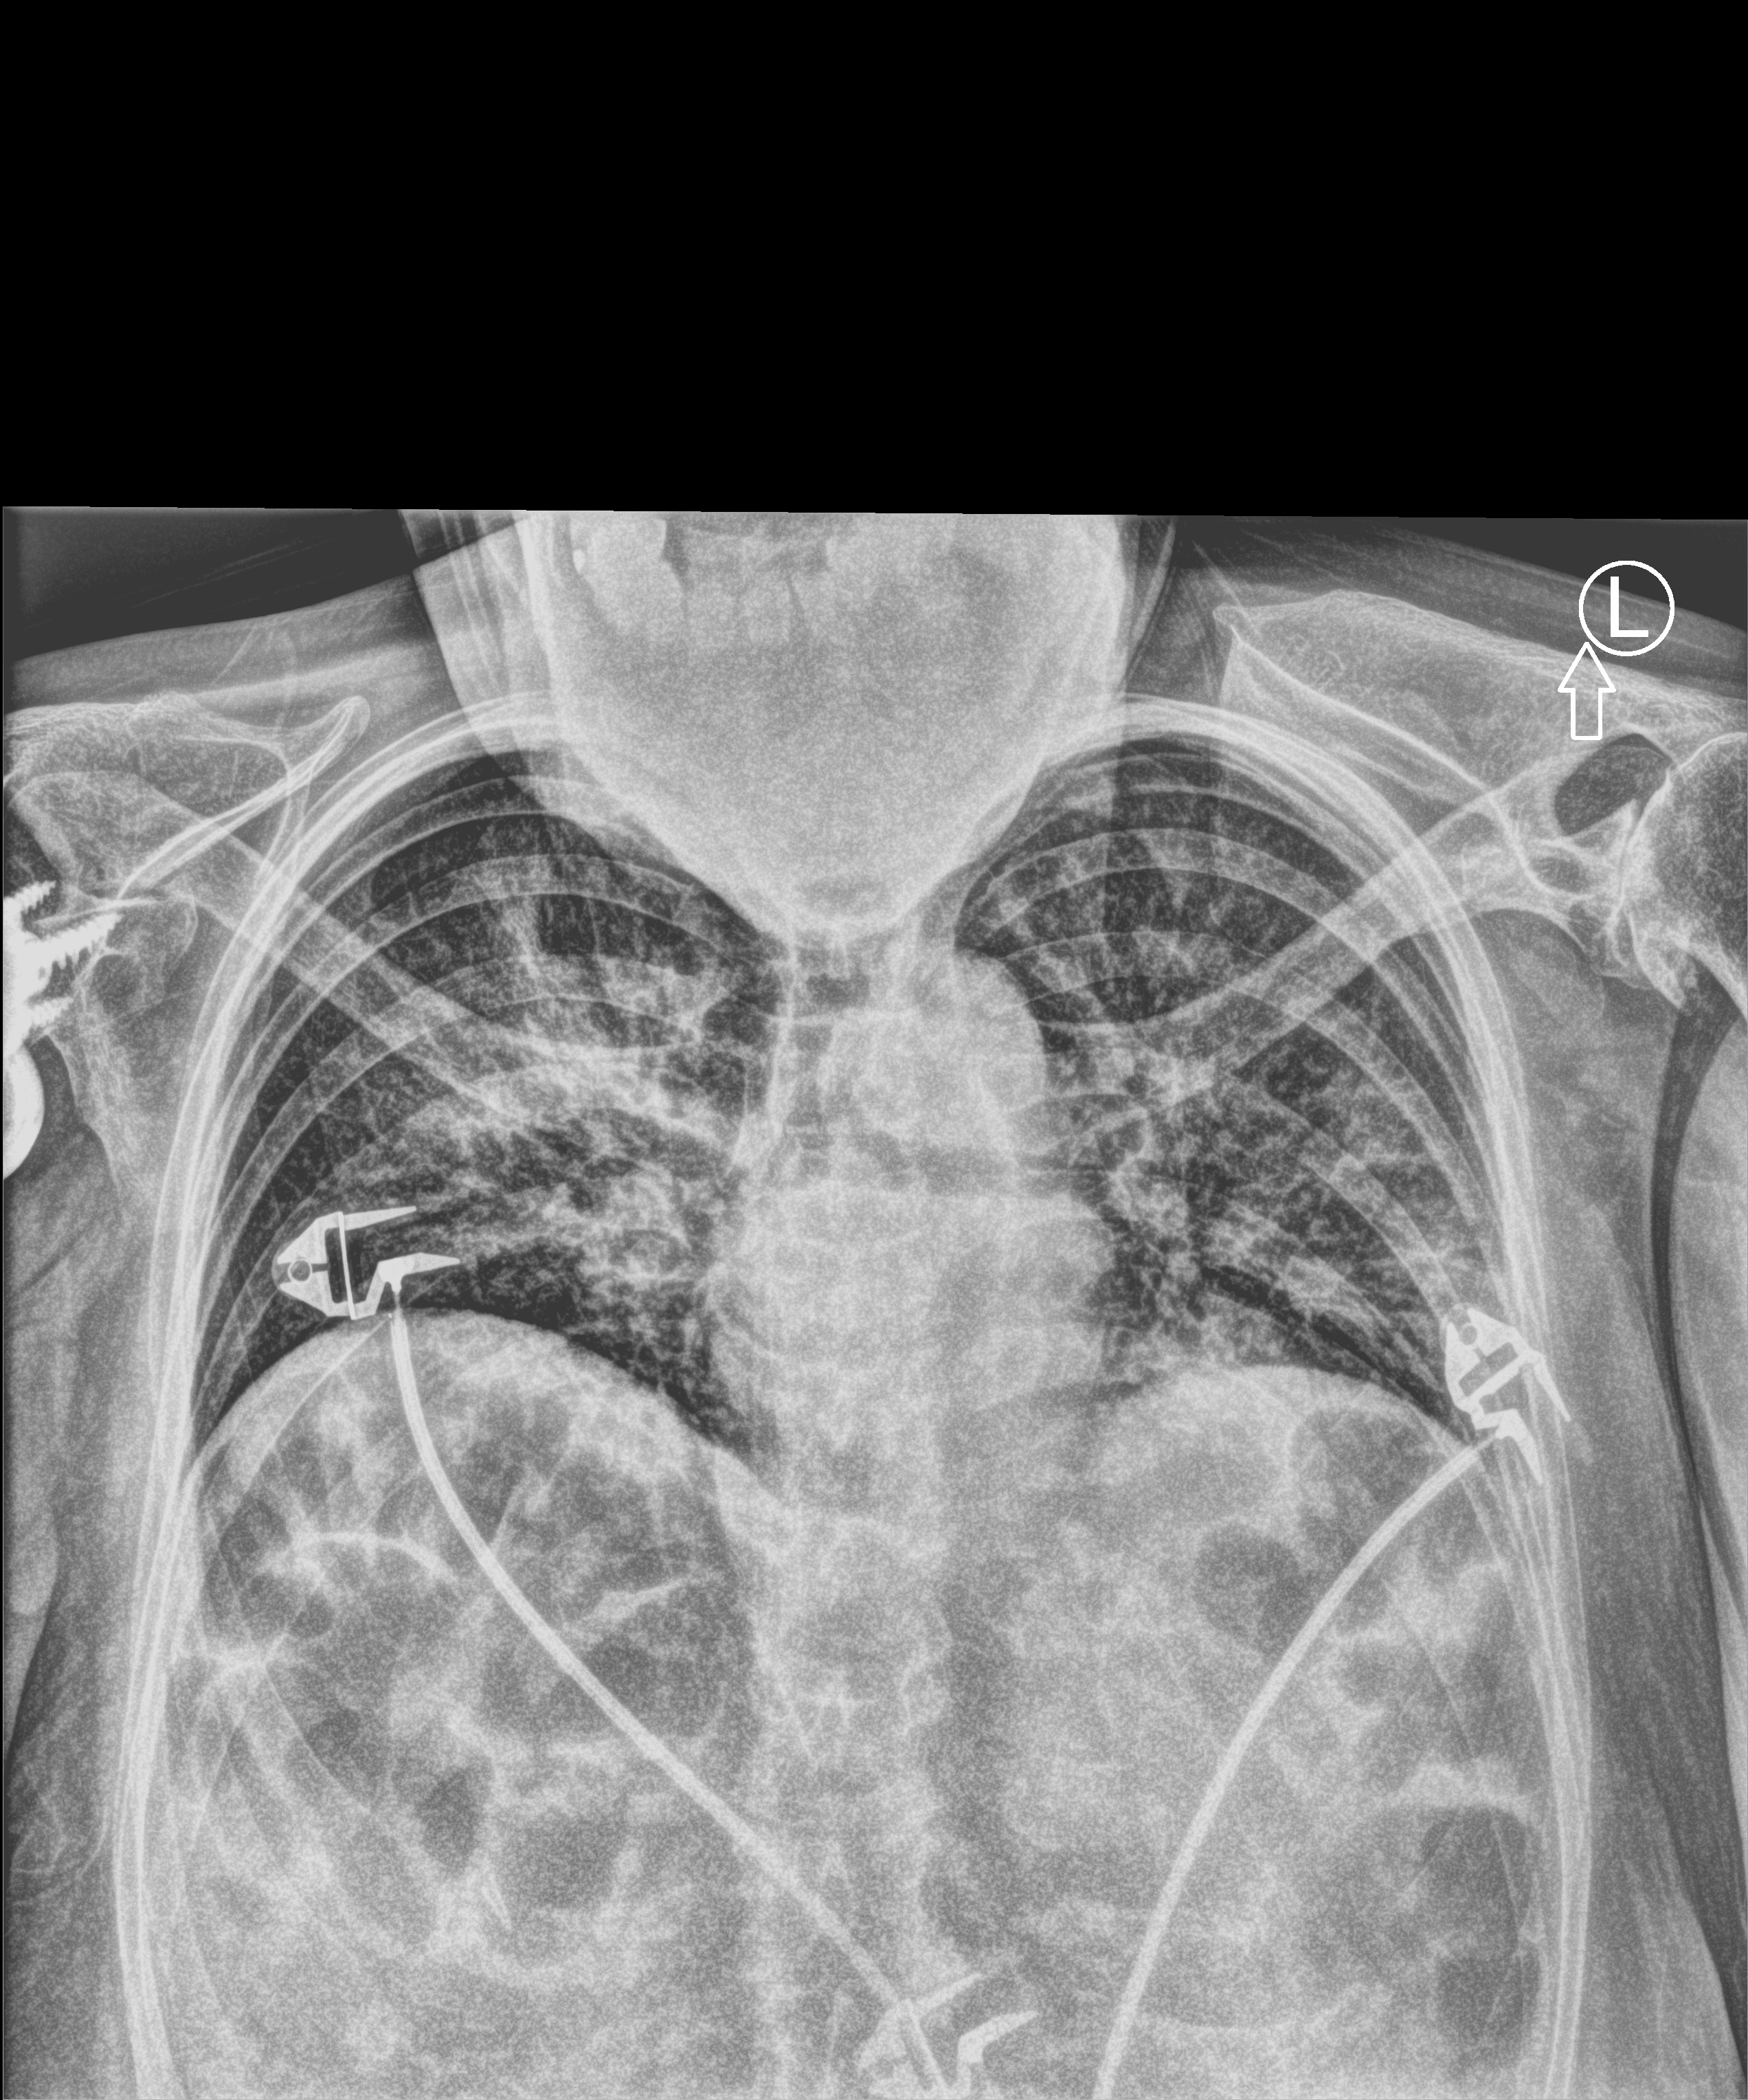
Chest X-ray (portable), anteroposterior (AP) projection. Female patient hospitalised with COVID-19, age 60–74 years.
Hospital-stay facts (about this admission, not read from this image; timing relative to this image not recorded):
- mechanically ventilated during this hospital stay: yes